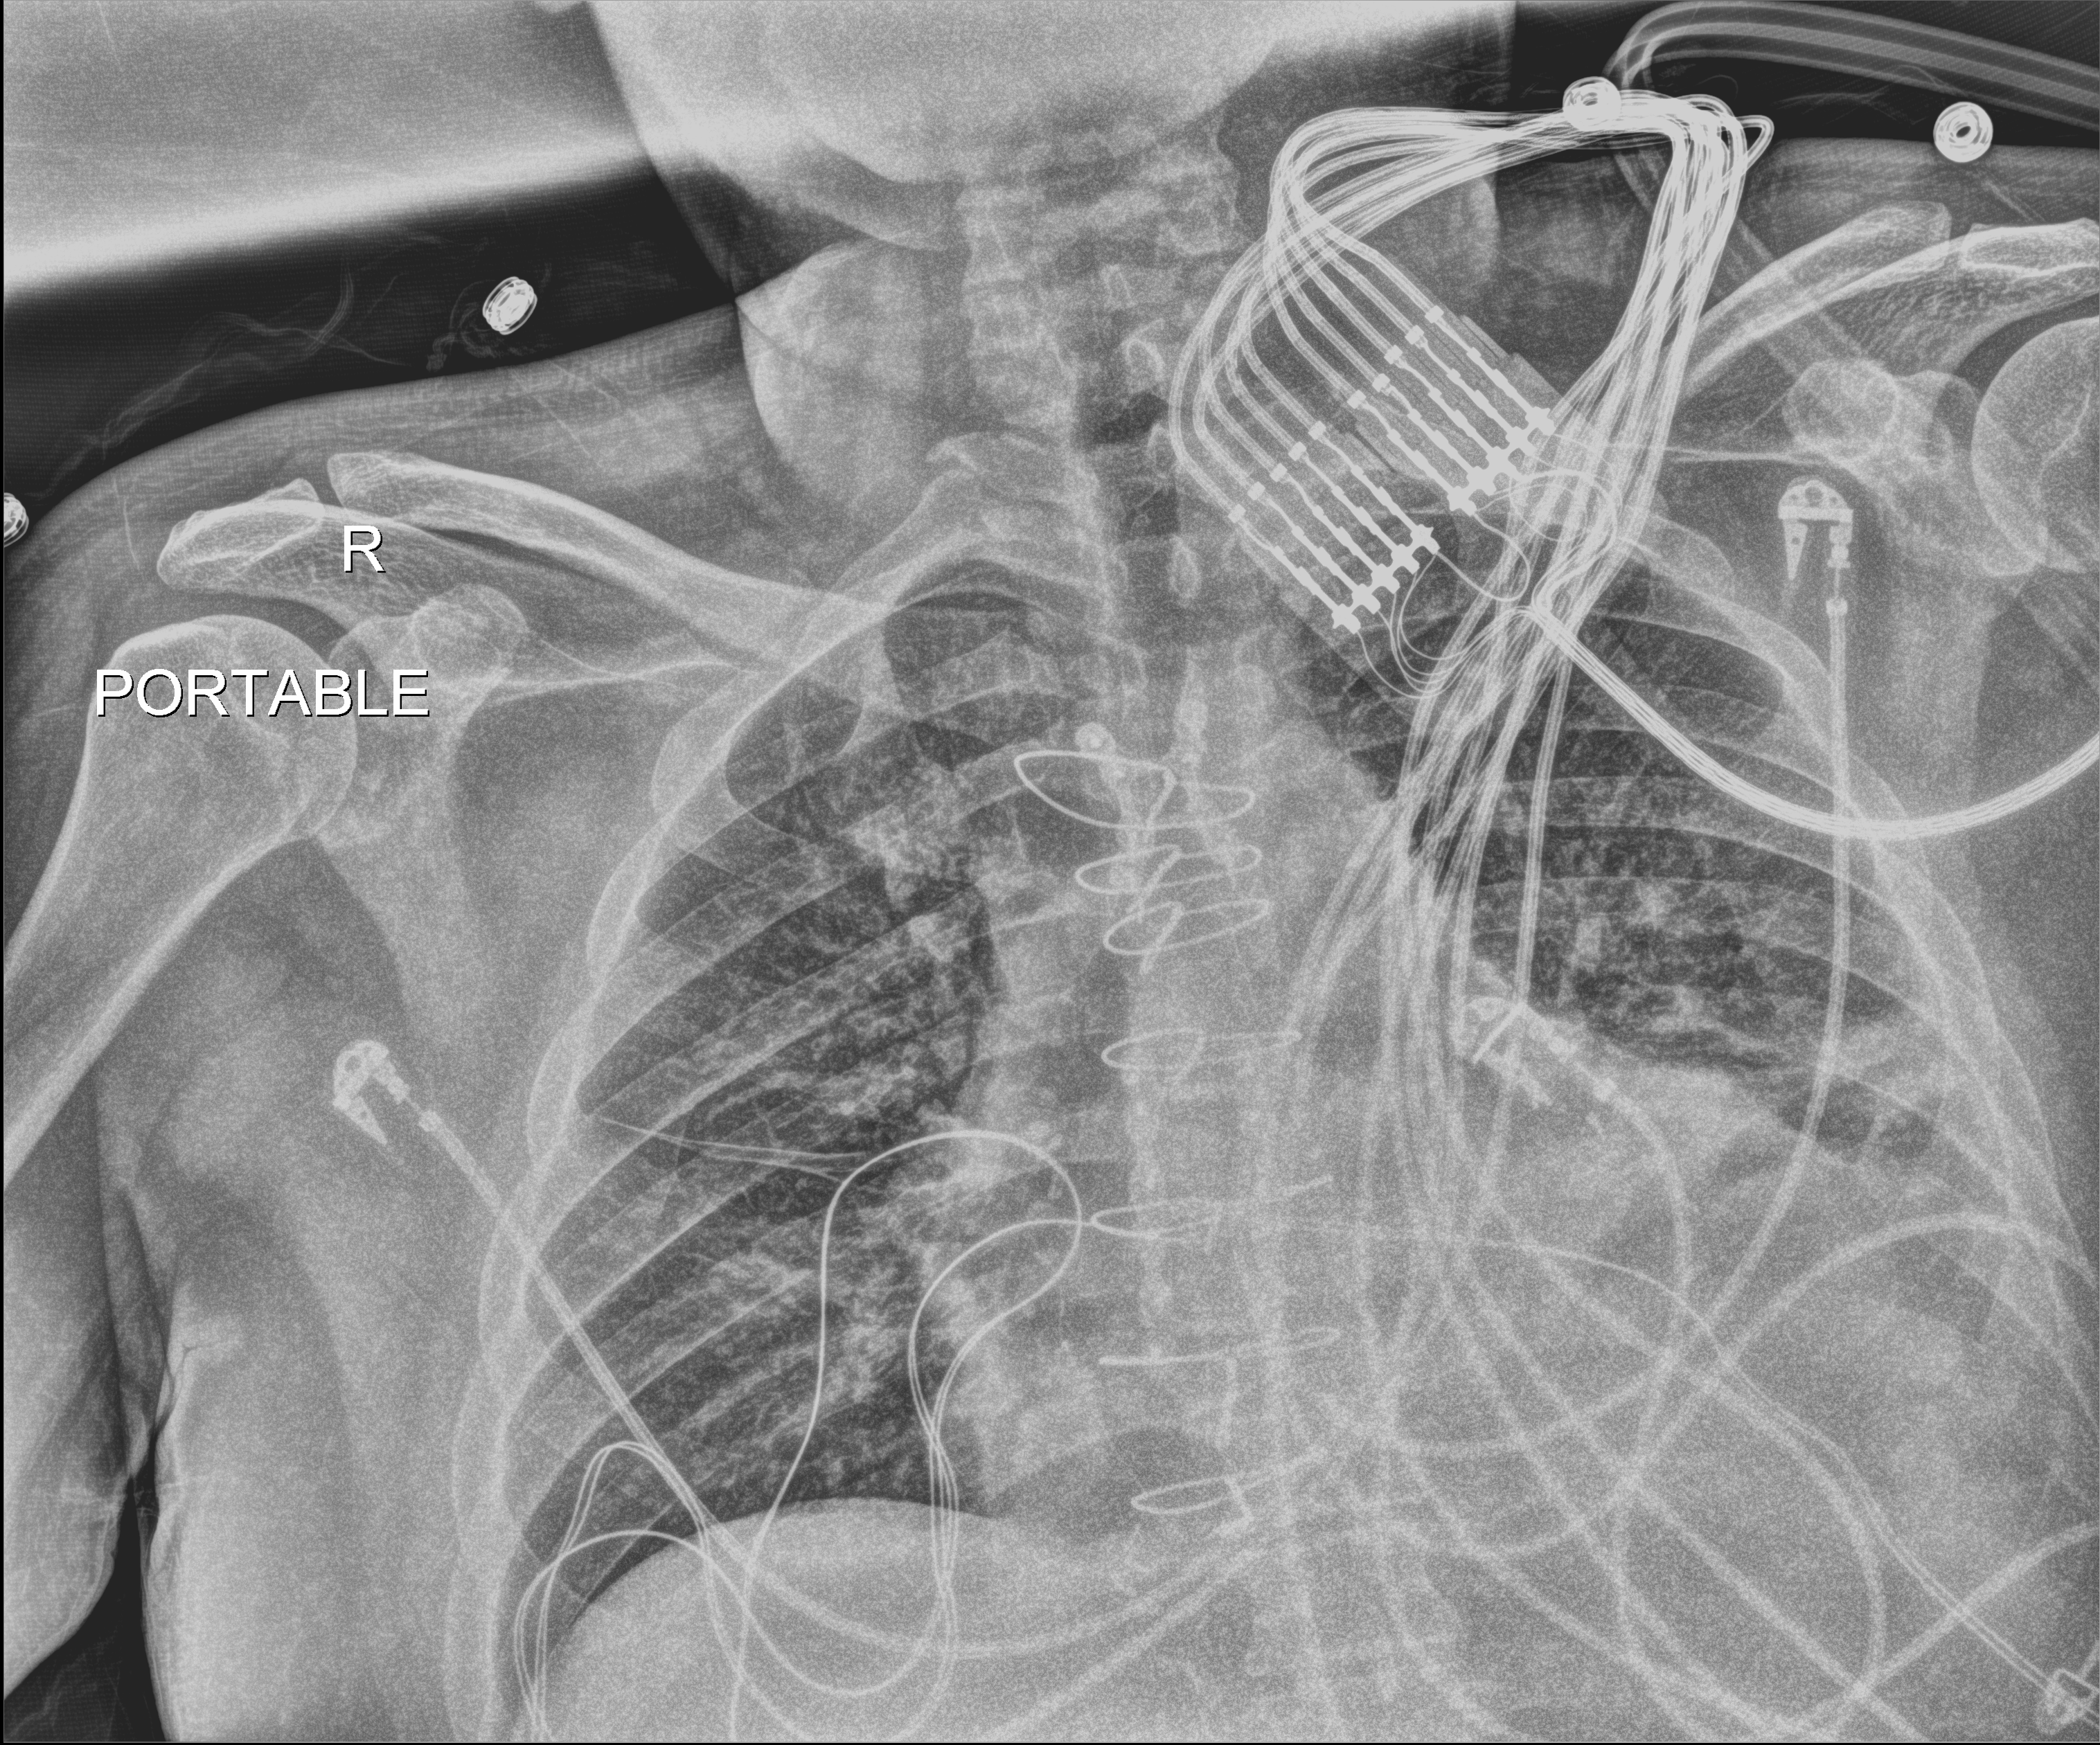
Chest radiograph. Patient hospitalised with COVID-19; male, aged 18–59 years.
Hospital-stay facts (about this admission, not read from this image; timing relative to this image not recorded):
- admitted to intensive care during this hospital stay: no